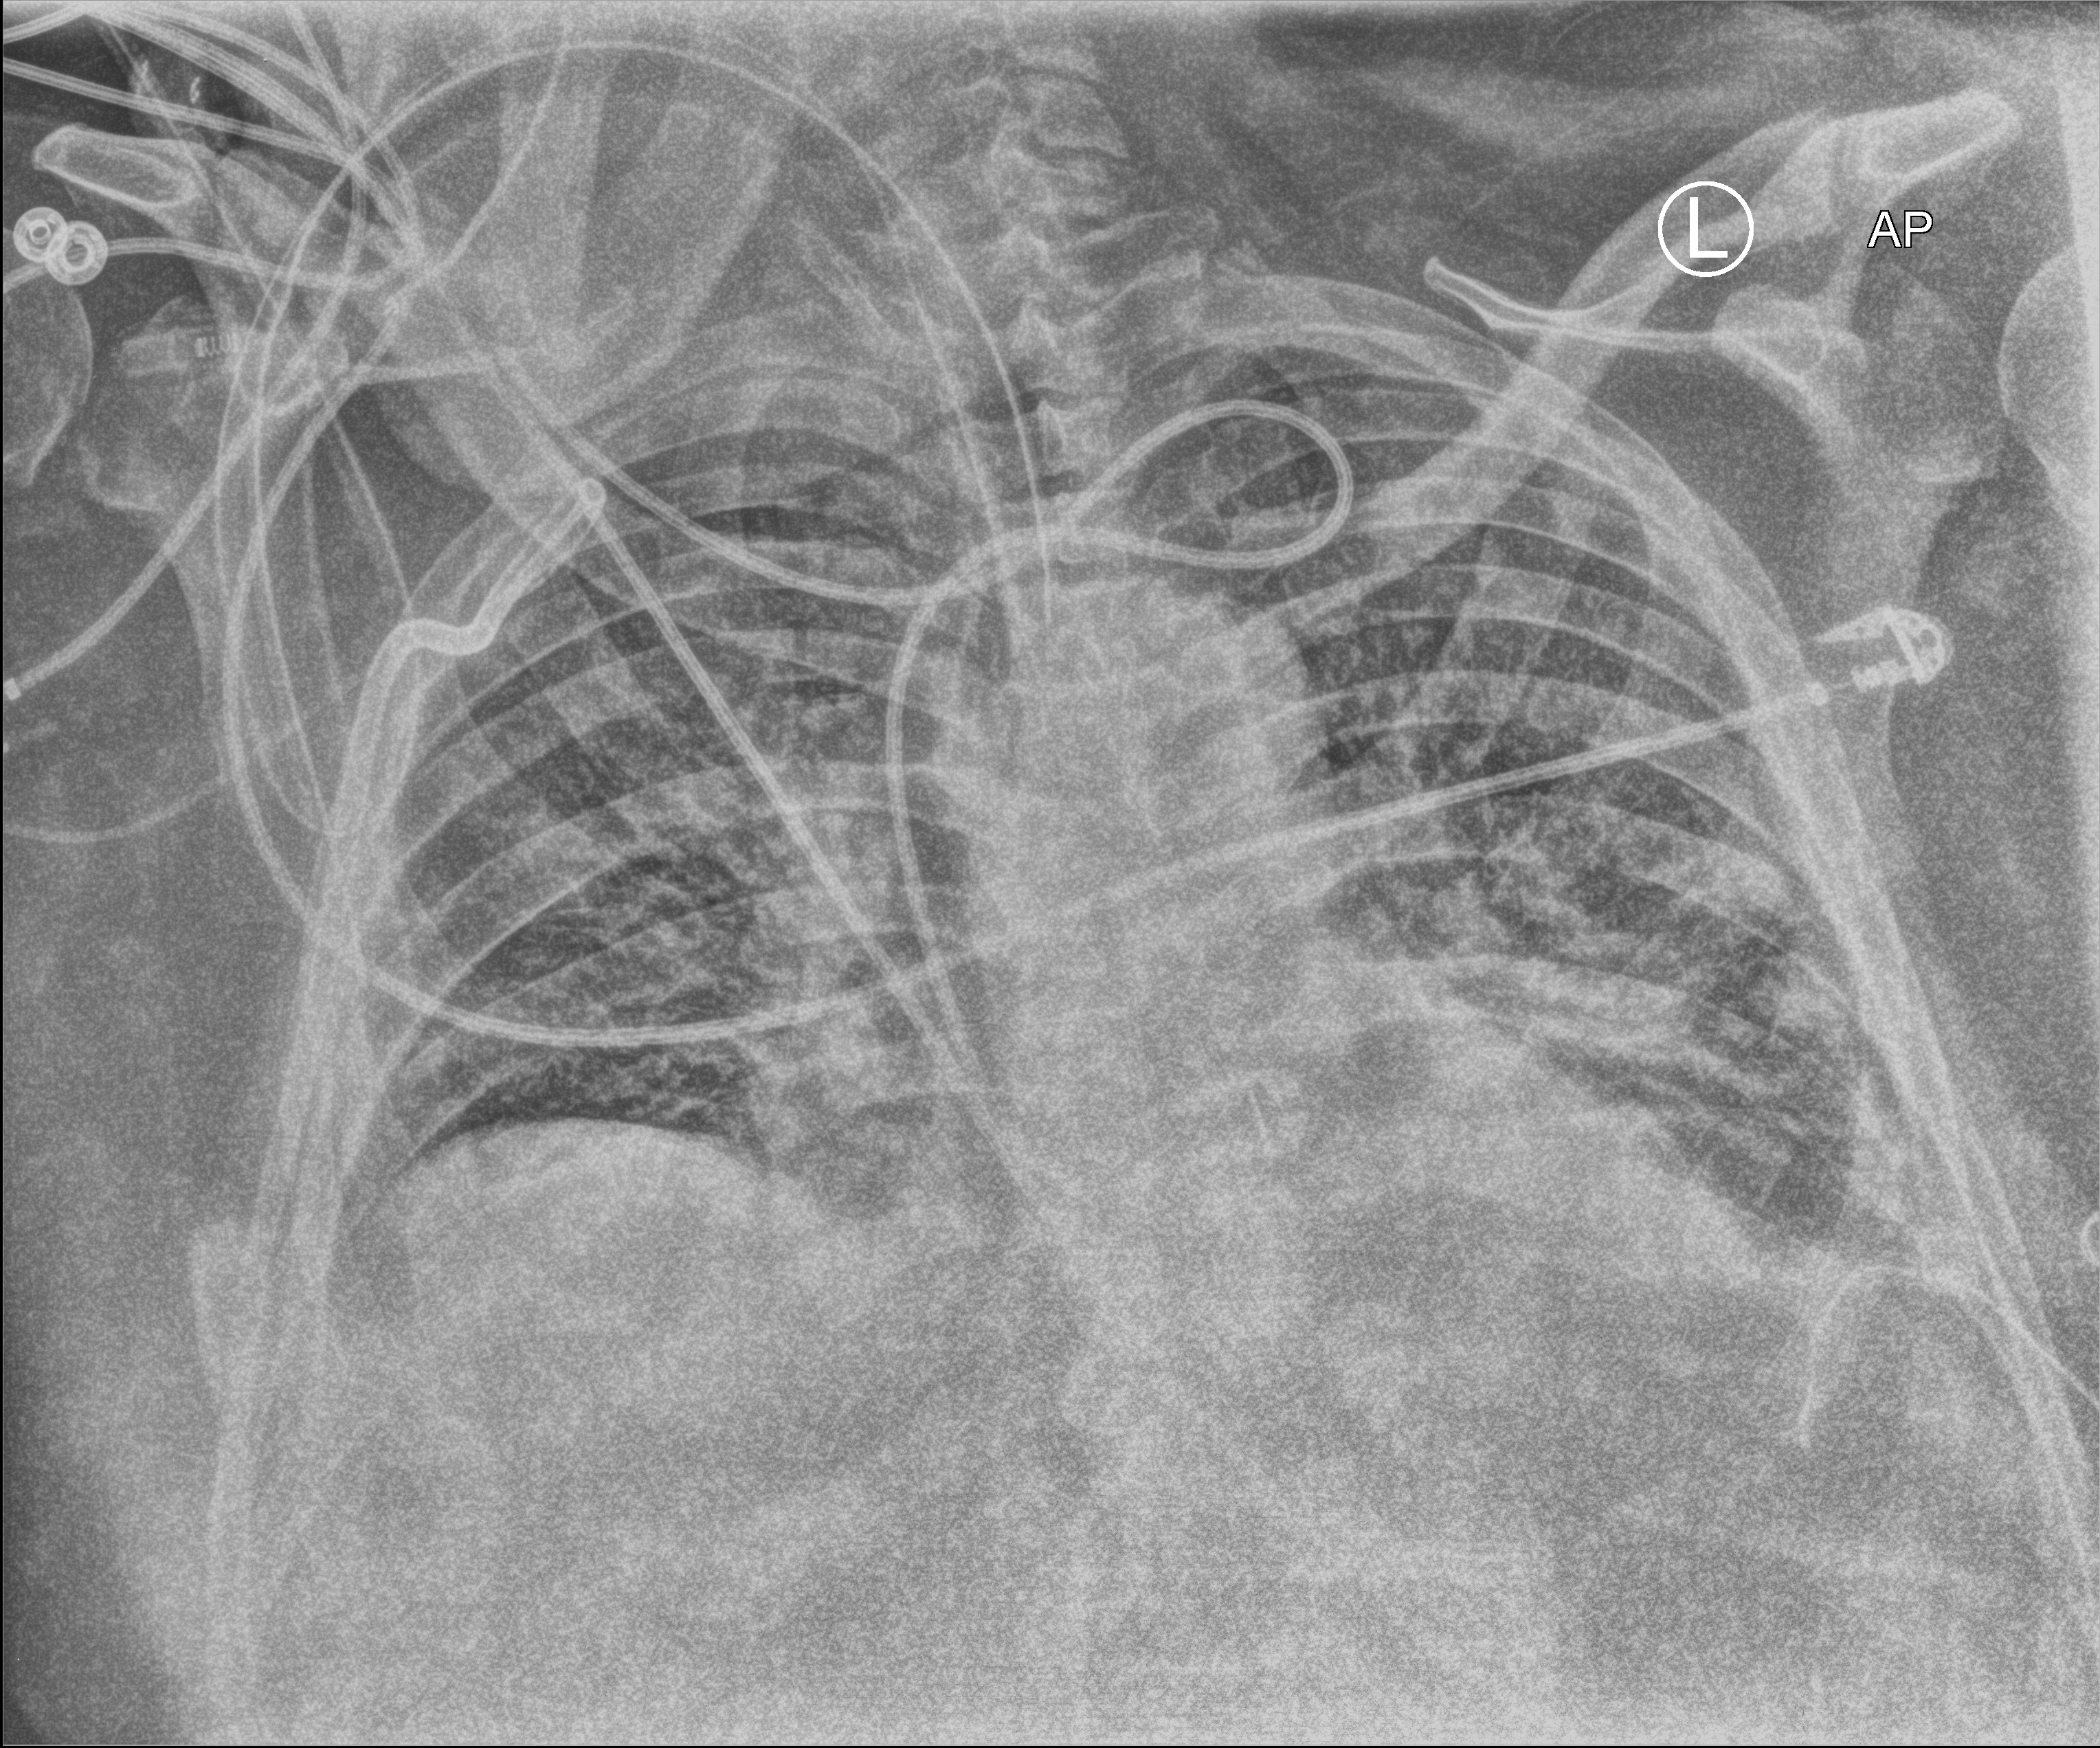
Chest X-ray (portable), anteroposterior (AP) projection. Male patient hospitalised with COVID-19, age 60–74 years.
Hospital-stay facts (about this admission, not read from this image; timing relative to this image not recorded):
- COPD (admission record): no
- admitted to intensive care during this hospital stay: yes